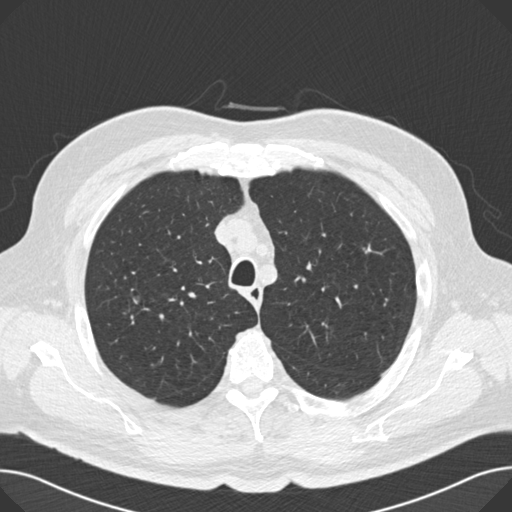
Low-dose screening chest CT, axial slice. Second screening round (one year after baseline). Lung window (W 1500 / L -600 HU). Standard (soft-tissue) reconstruction kernel (B30f). 120 kVp. Slice 38 of 166 in the series. Male, age 67 years at enrolment. Current smoker at enrolment.
Expert reader's lesion annotation, box from (x=127, y=291) to (x=145, y=311) px. Screening reader's record for this exam: no non-calcified nodule ≥4 mm recorded. Participant outcome: lung cancer diagnosed 194 days after this screen — small cell carcinoma, NOS, right middle lobe, stage IA (AJCC 6th edition), 20 mm at pathology.